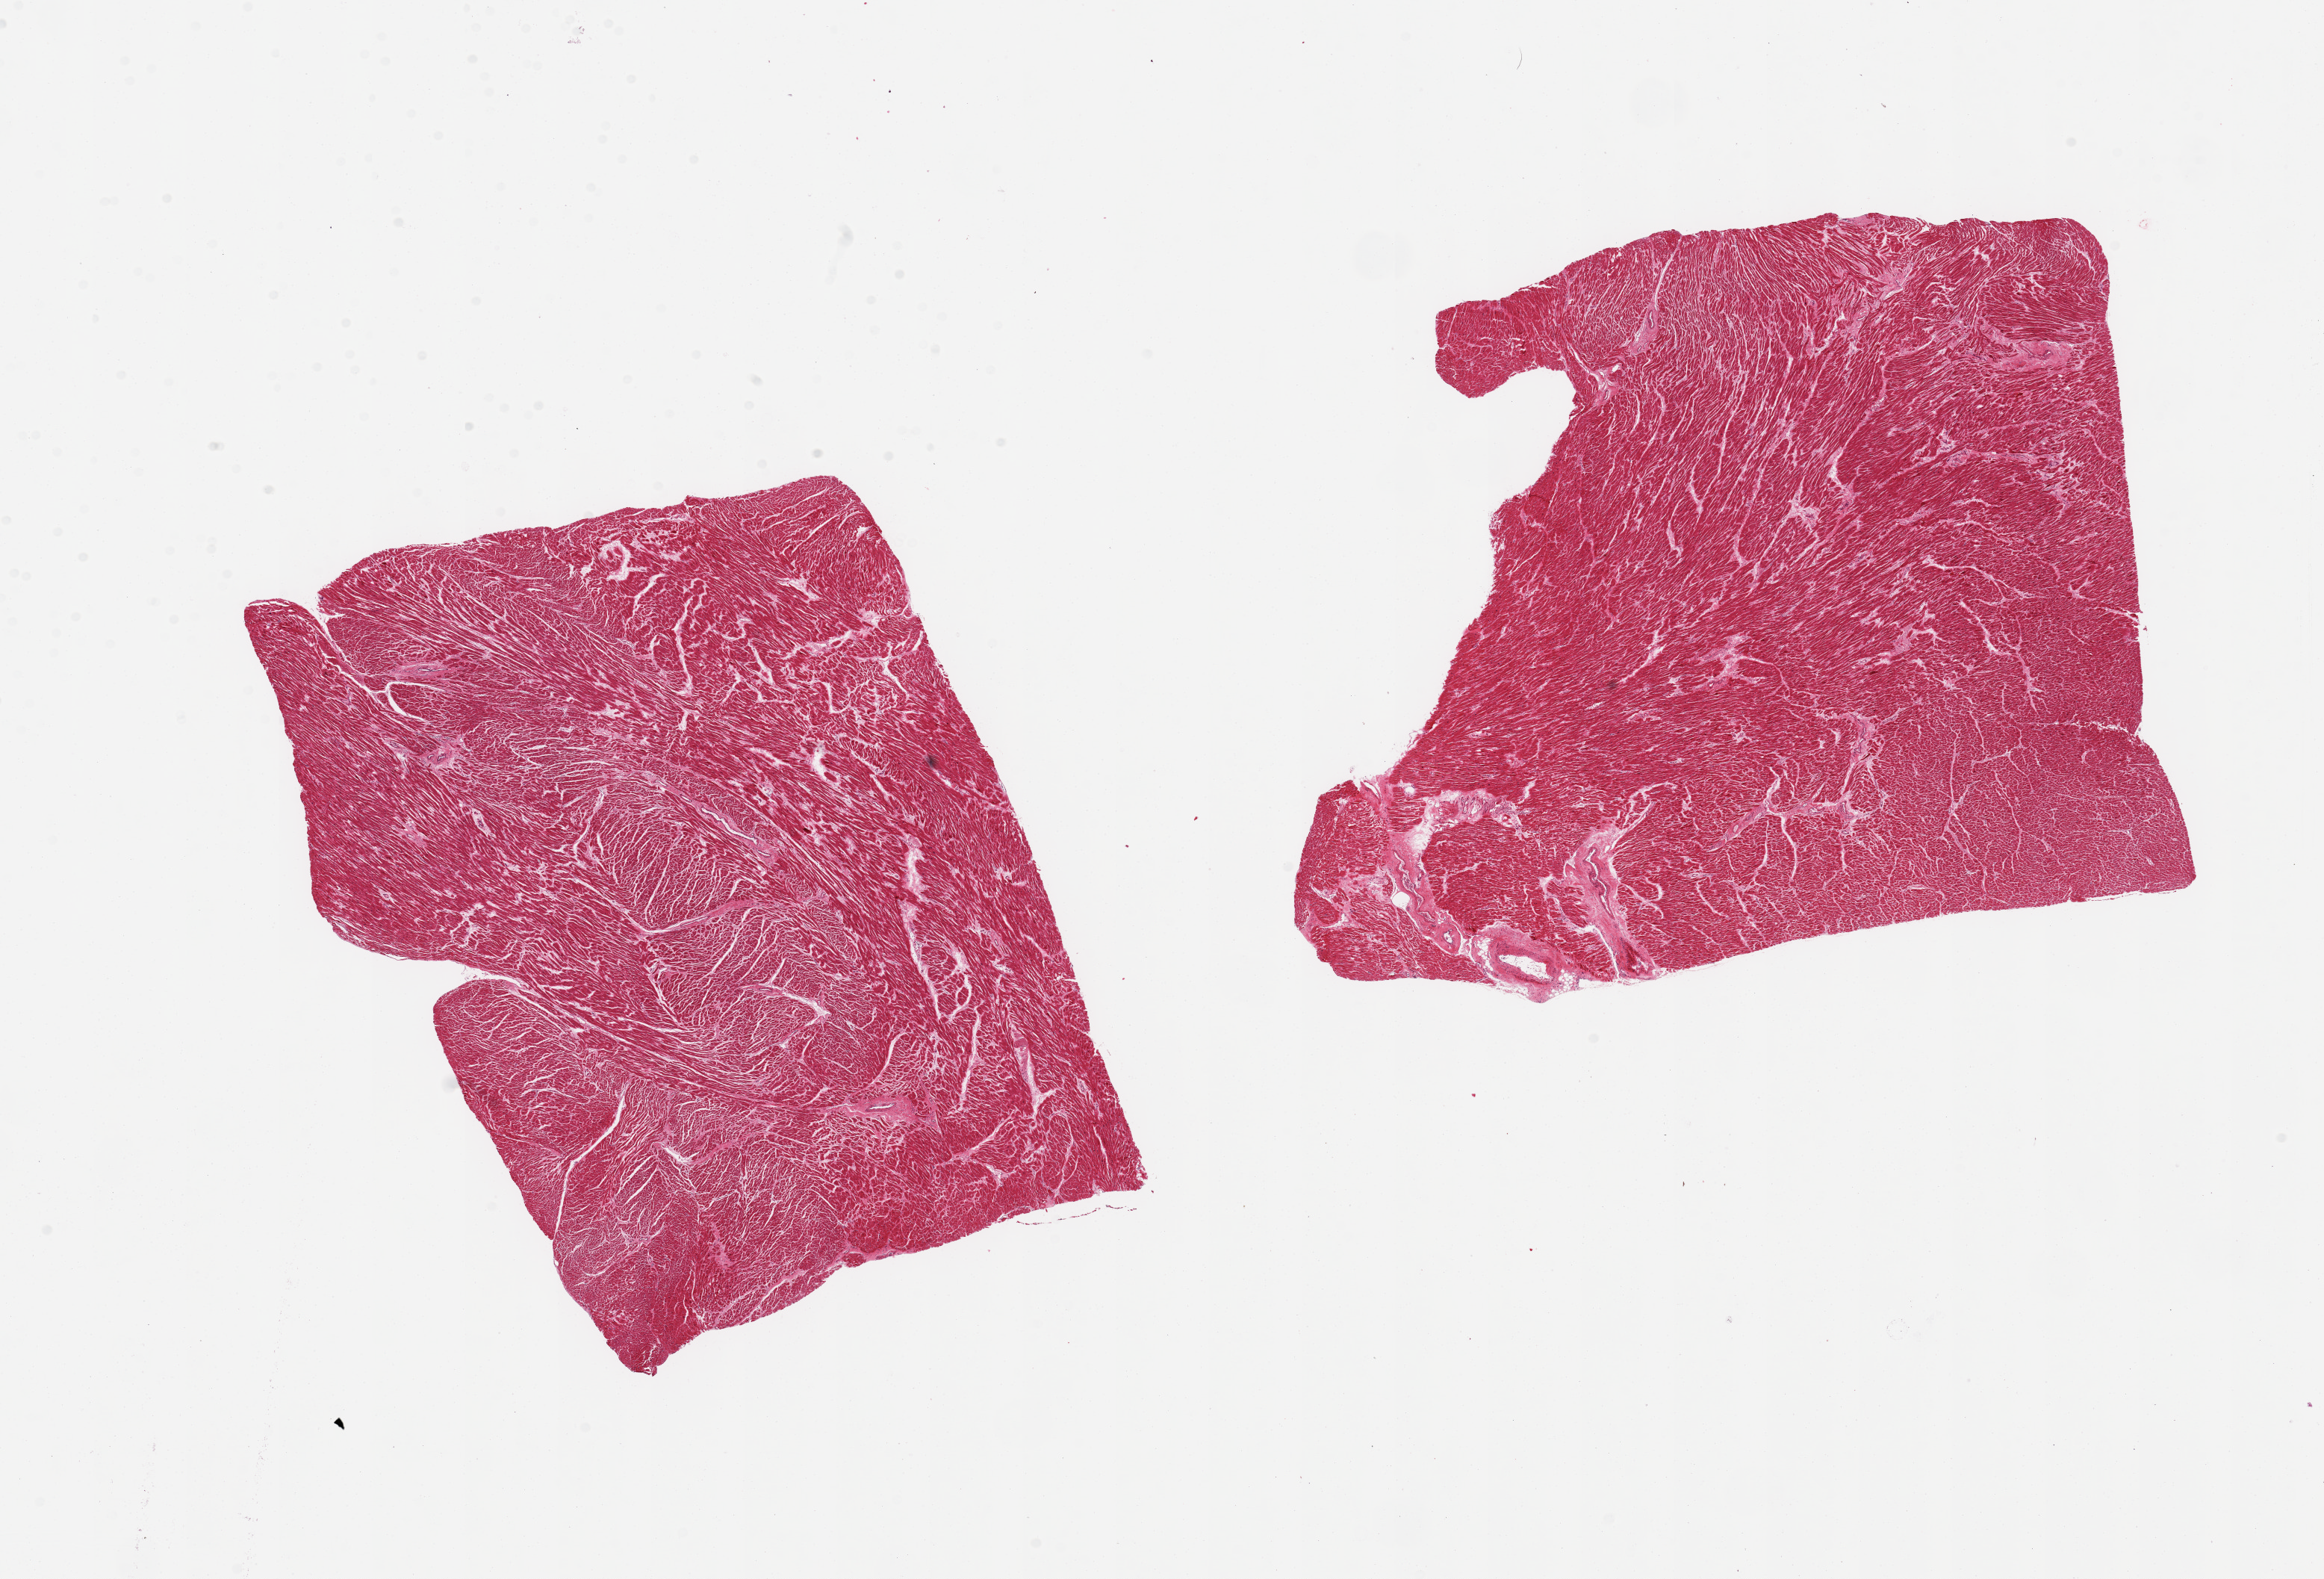
Digitized H&E-stained section, shown as a low-resolution overview of the whole scanned area (about 24.6 x 16.7 mm); PAXgene-fixed, paraffin-embedded tissue; section of heart (target tissue); tissue donor sample.
- review note (as recorded): 2 pieces, moderate chronic ischemic changes/interstitial fibrosis